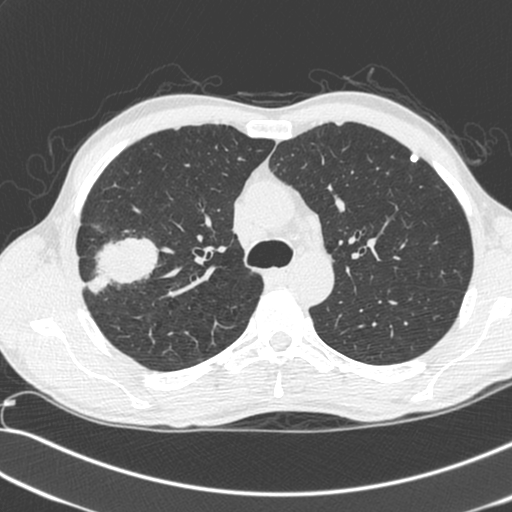
Low-dose screening chest CT, axial slice, first (baseline) screen, lung window (W 1500 / L -600 HU), 1.3 mm slice thickness, 512 × 512 image matrix. Male, age 55 years at enrolment. Current smoker at enrolment.
- Expert-annotated lung lesion, bounding box (x1, y1, x2, y2) in pixels: (71, 233, 152, 306).
- Reader record for this screening exam (exam-level; its link to the box is not recorded): non-calcified nodule or mass ≥4 mm, right upper lobe, 52 × 39 mm, spiculated (stellate) margins, soft tissue attenuation.
- Official screen result: positive, change unspecified: nodule(s) >= 4 mm or enlarging nodule(s), mass(es), or other non-specific abnormalities suspicious for lung cancer.
- Participant outcome: lung cancer diagnosed 25 days after this screen — large cell neuroendocrine carcinoma, right upper lobe, poorly differentiated (G3), stage IIB (AJCC 6th edition), 49 mm at pathology.